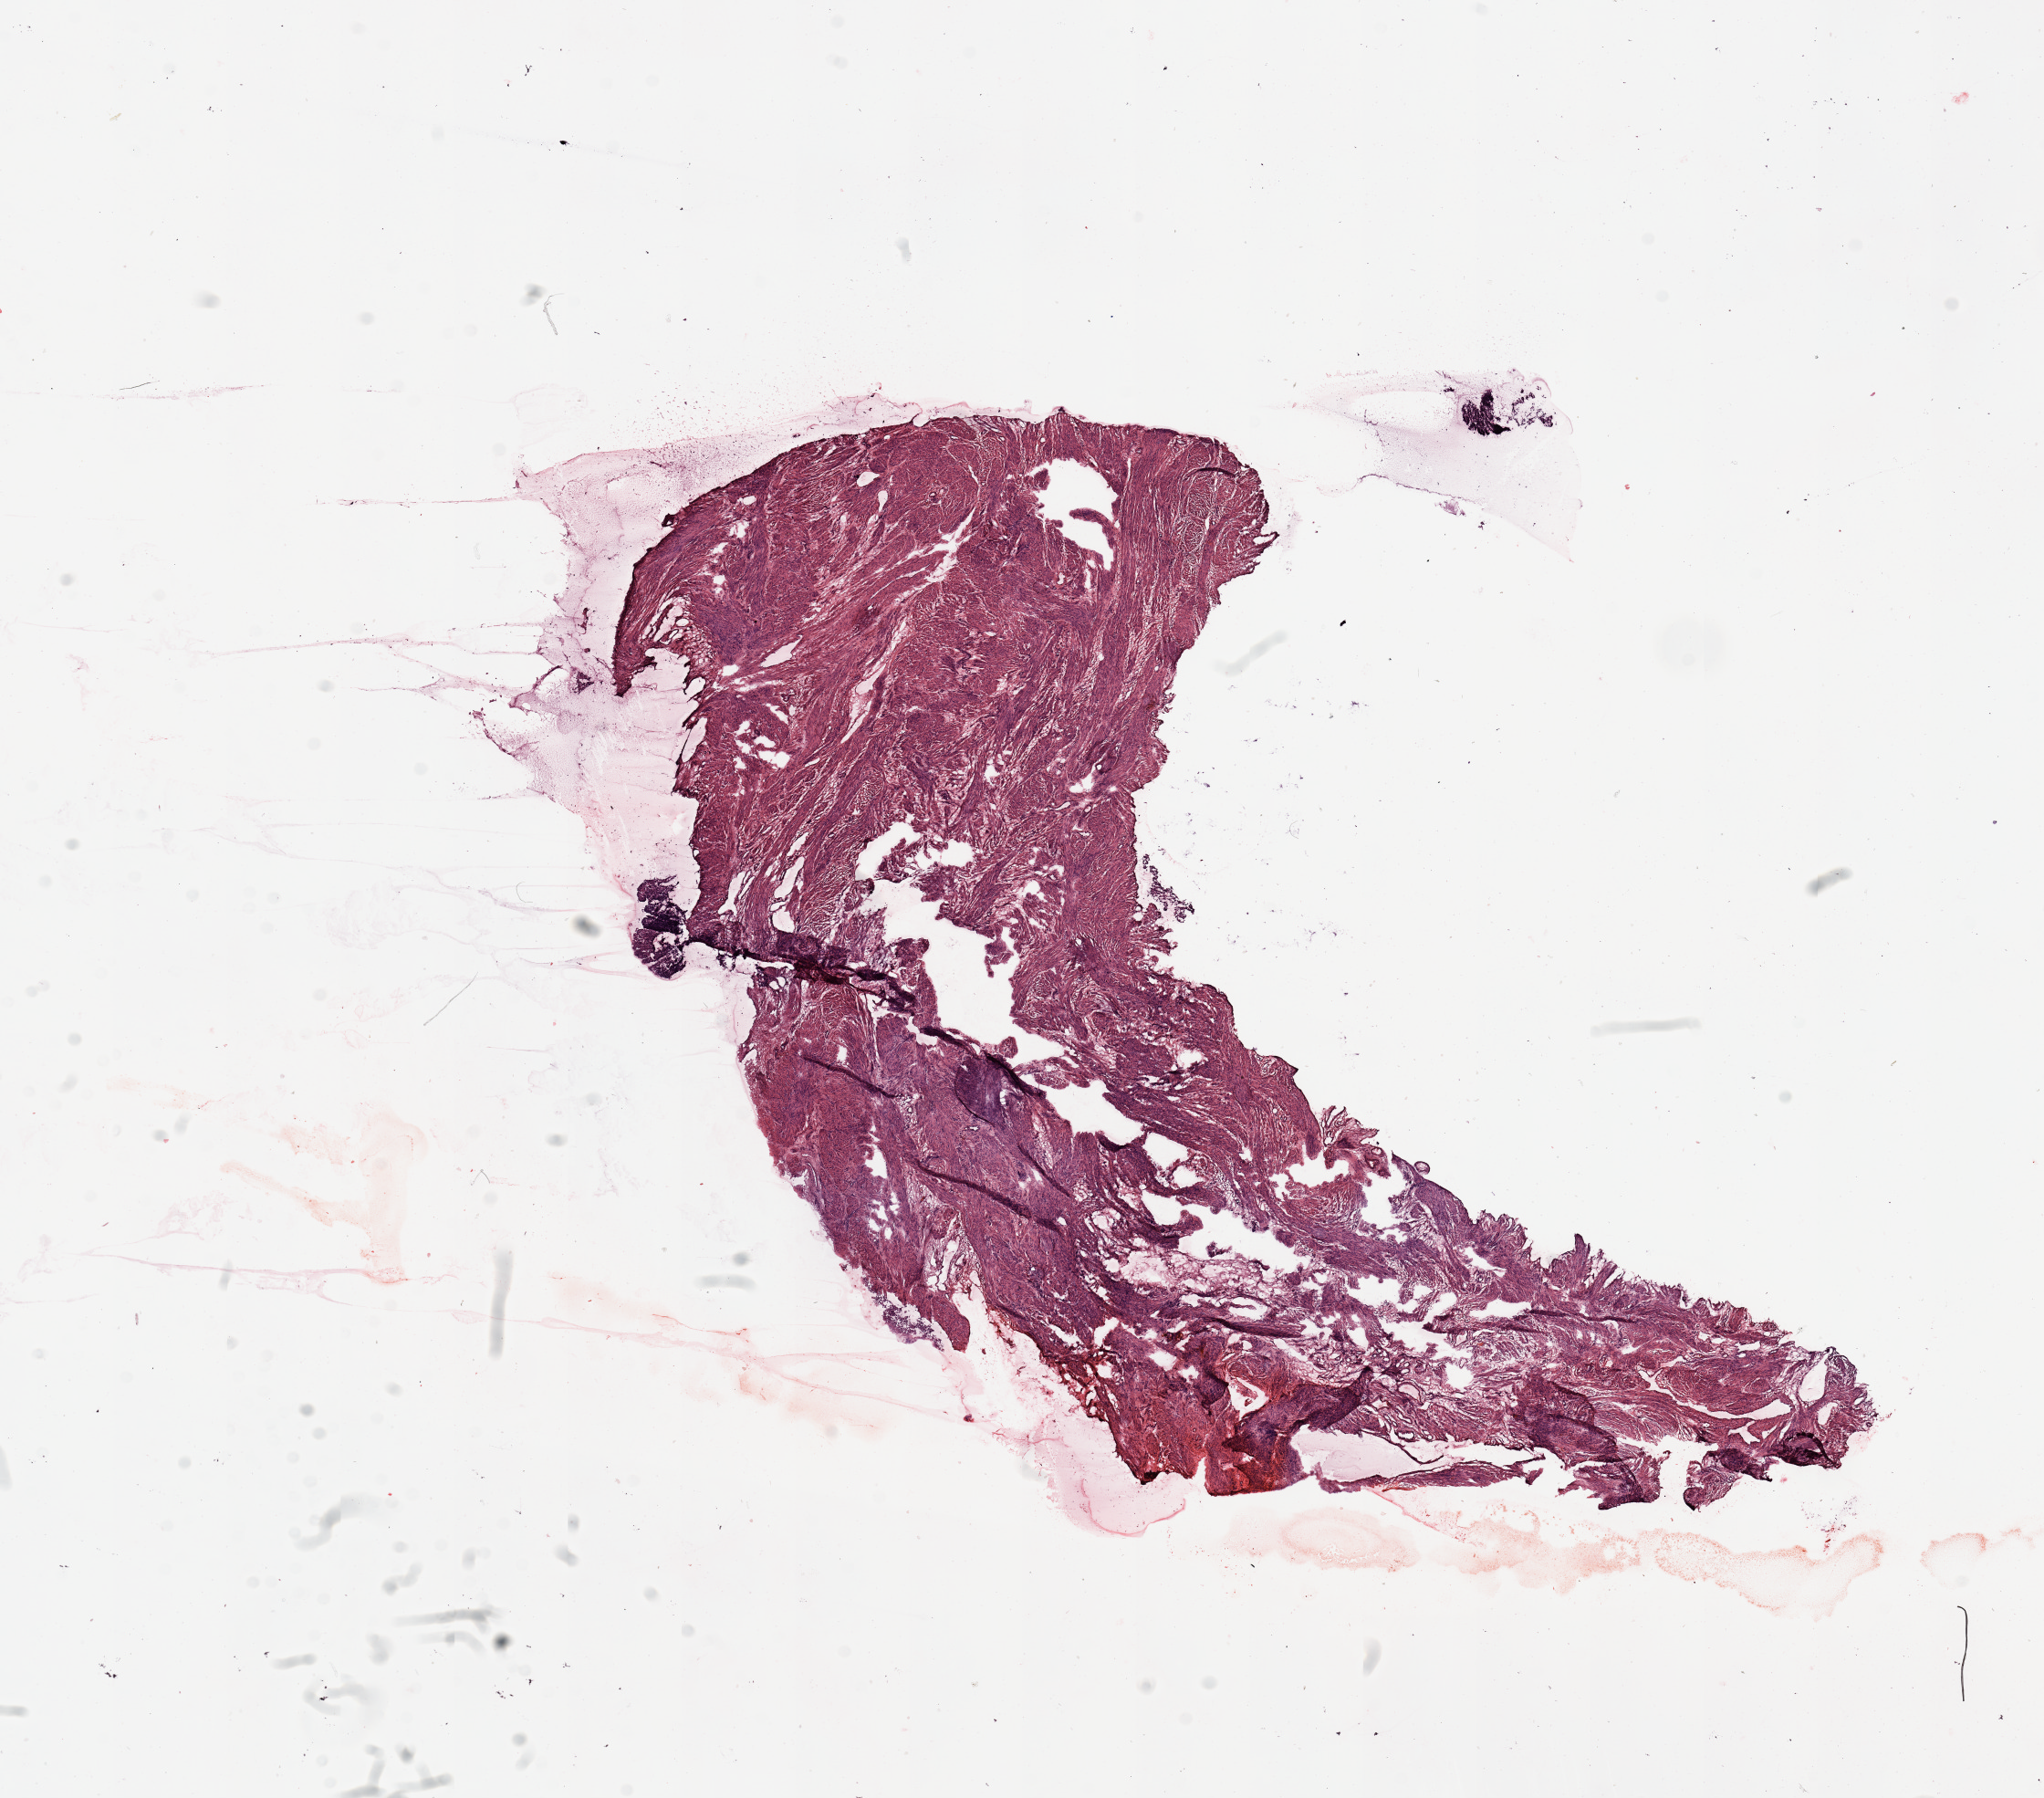
Digitized H&E-stained tissue section (whole slide) — a low-resolution overview of the entire scanned area, about 17.7 x 15.6 mm (slide scanned at 20x). Normal (non-tumour) tissue sample, uterus. 45-year-old female patient.
This section: normal (non-tumour) tissue from the same patient. Patient diagnosis: Endometrioid adenocarcinoma, NOS.